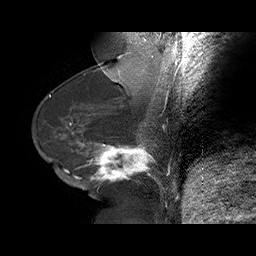
Breast MRI (dynamic contrast-enhanced), one sagittal slice; position 29 of 75 along the scan axis; dynamic contrast-enhanced series, time point 2 of 6 at this slice position (early post-contrast); 1.5 T; TE 4.5 ms, TR 32.4 ms; 3 mm slice thickness; 256 × 256 image matrix, field of view 180 × 180 mm. Female patient. Case-level facts recorded for this patient, not image findings: setting: breast cancer imaged before/during neoadjuvant chemotherapy; receptor status: HR-positive, HER2-negative.
Annotated regions visible in this slice (semi-automatic segmentation, software-assisted and operator-edited):
- analysis volume of interest (the breast-tissue region the enhancement analysis was run in; not a lesion): box from (x=58, y=134) to (x=166, y=191) px
- tumour enhancement mask (voxels above the 100 % enhancement threshold inside the analysis volume of interest): (x=63, y=142)–(x=152, y=182)